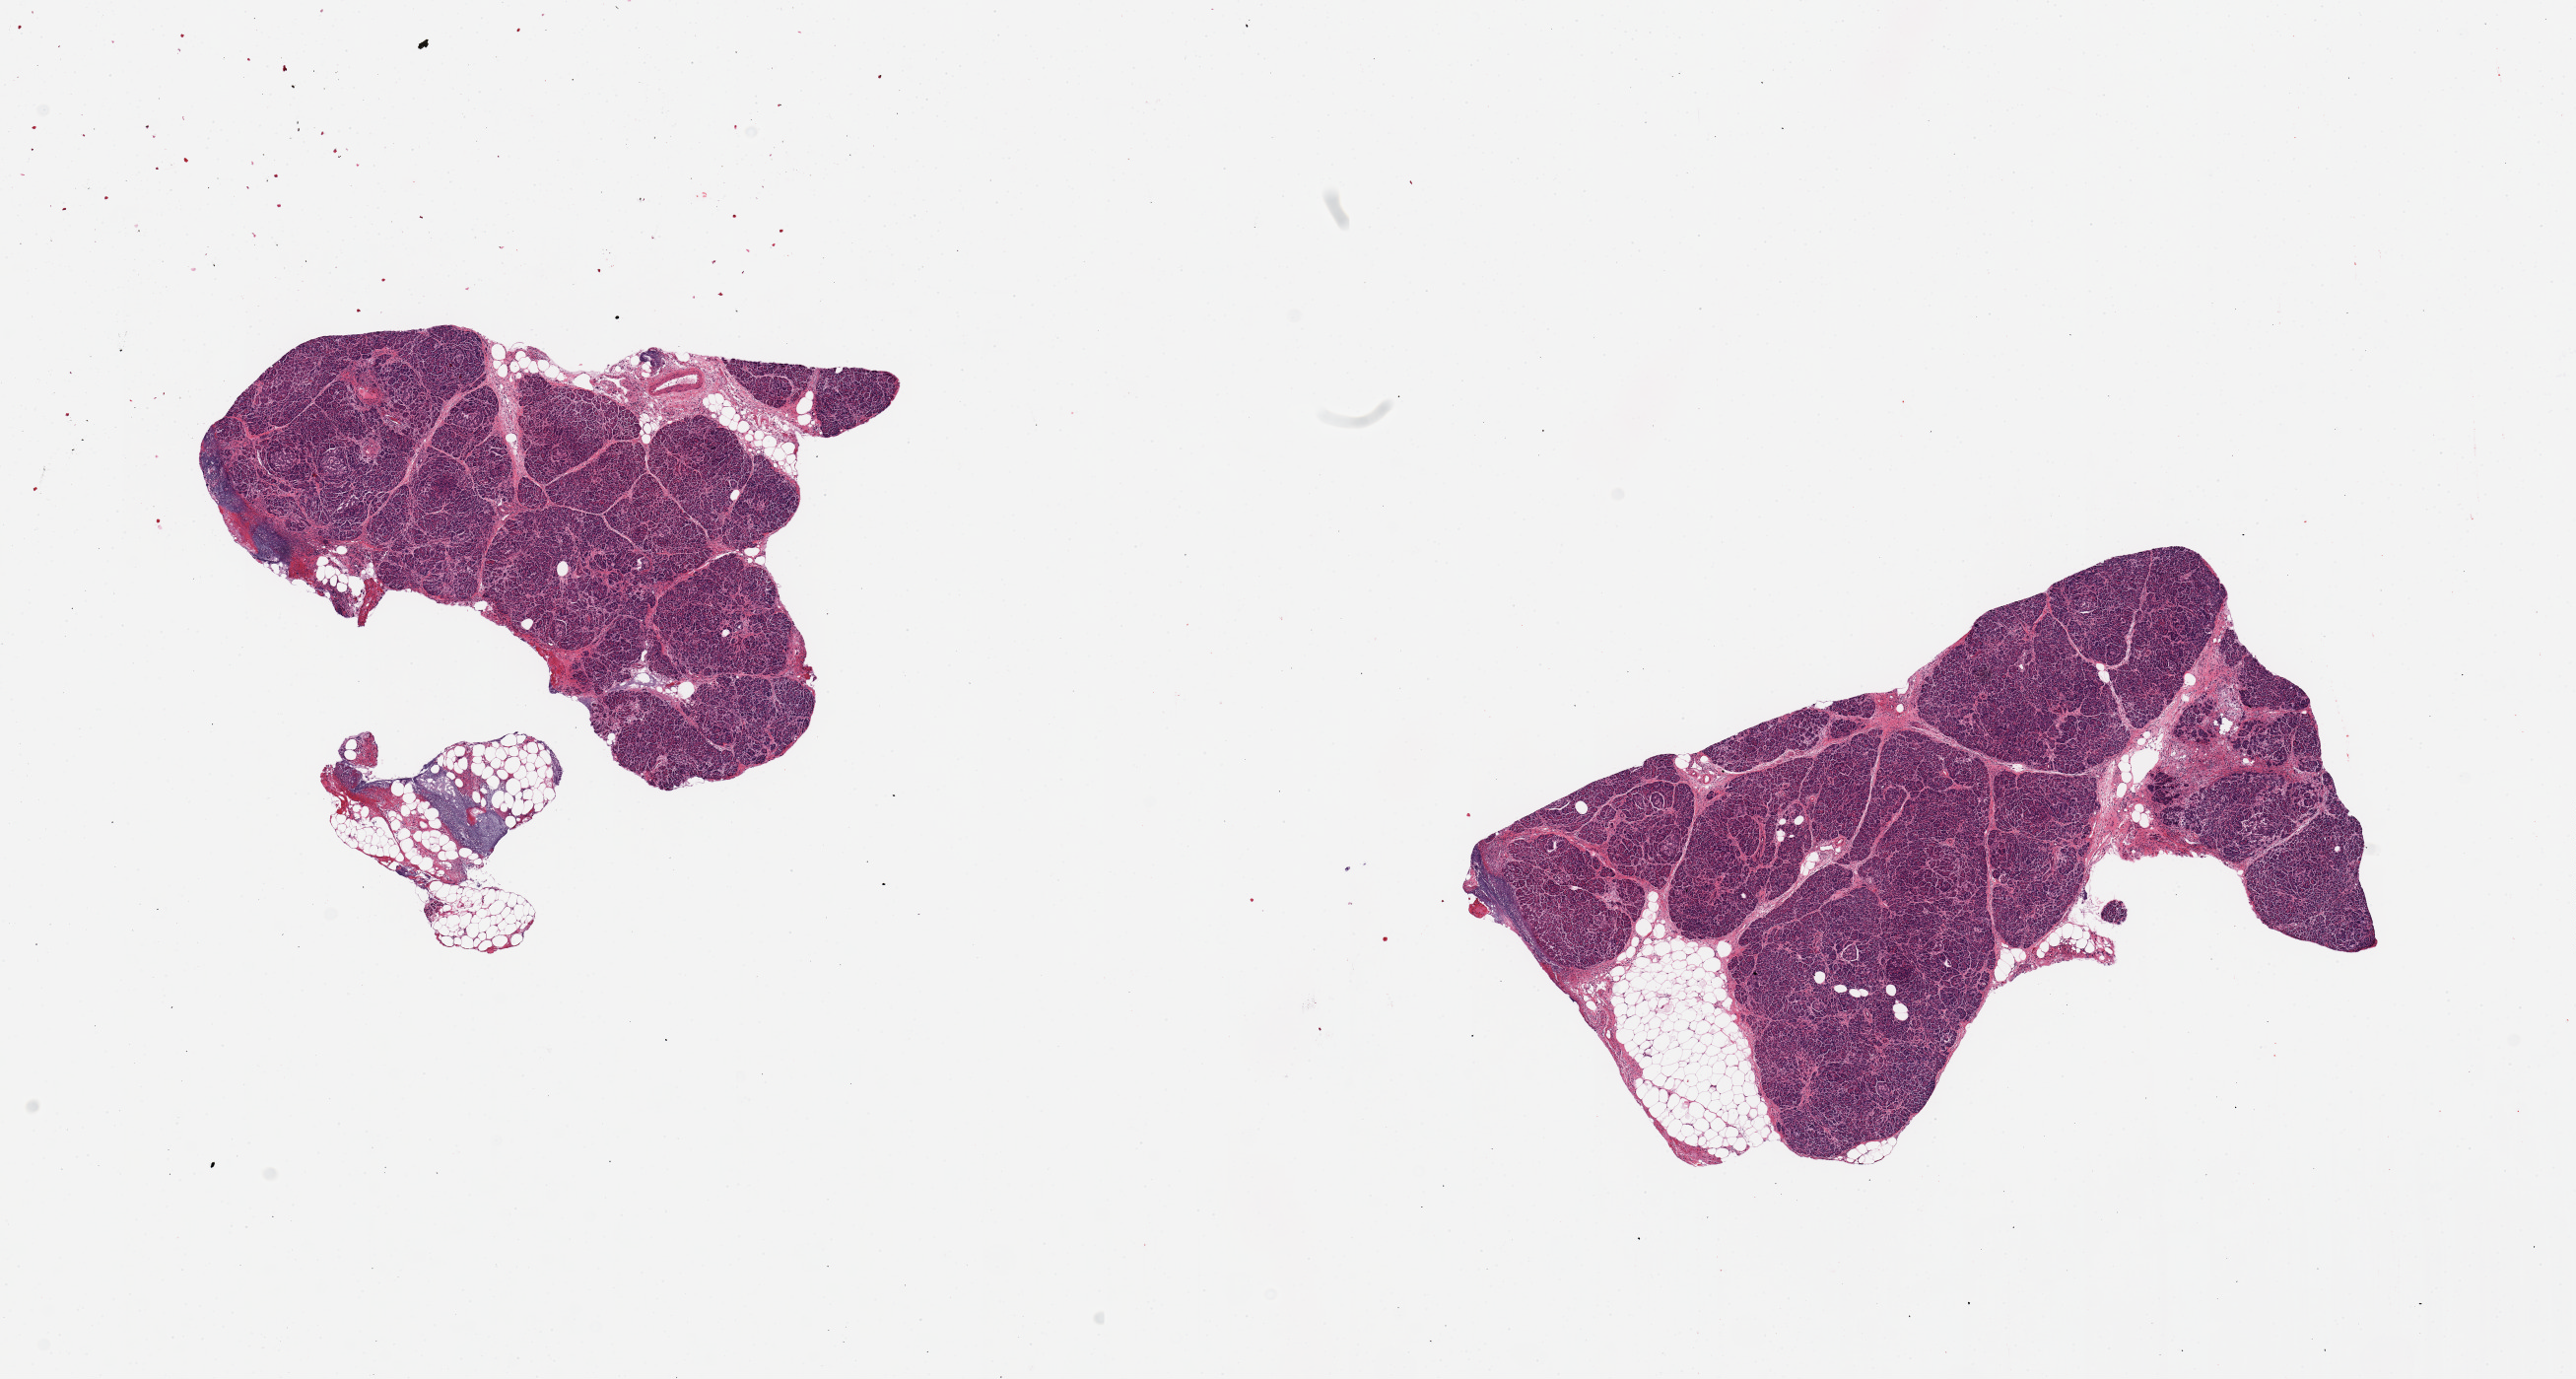
Whole-slide image, haematoxylin and eosin stain, shown as a low-resolution overview of the whole scanned area (about 20.7 x 11.1 mm, acquisition: 20x scan); PAXgene-fixed, paraffin-embedded tissue; target tissue: pancreas; tissue donor sample. Donor sex: female.
- reviewer comment on this tissue sample: 2 pieces, acute pancreatitis